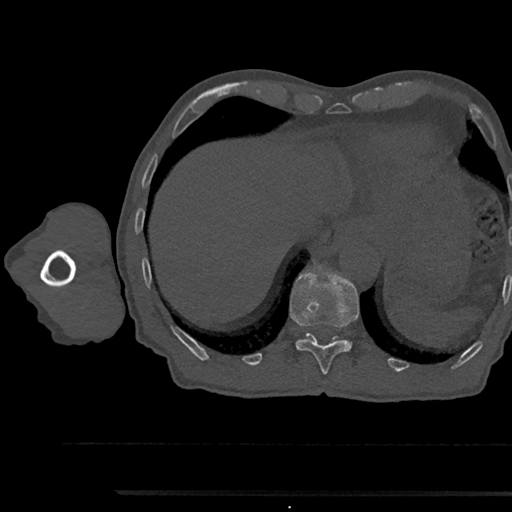
CT including the spine, one axial slice; position 774 of 797 along the scan axis; reconstruction kernel Br40s/3; 120 kVp; bone window (W 1800 / L 400 HU); 512 × 512 image matrix. Male patient, age 79 years. From the clinical record (not read from this slice): primary cancer: prostate.
Structures marked on this image (semi-automatic segmentation, software-assisted and operator-edited):
- T11 vertebra: bounding box [x1, y1, x2, y2] px = [290, 266, 359, 375]